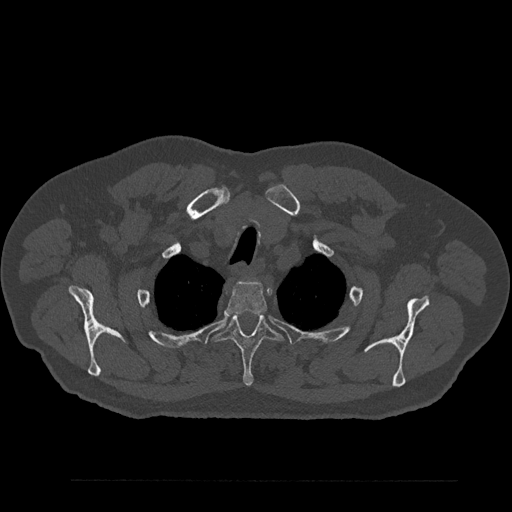
CT including the spine, one axial slice; position 695 of 797 along the scan axis; reconstruction kernel Br40s/3; 120 kVp; bone window (W 1800 / L 400 HU); 0.5 mm slice thickness; 512 × 512 image matrix, field of view 430 × 430 mm. Patient: male, 61 years. Case-level facts recorded for this patient, not image findings: primary cancer: prostate.
Structures marked on this image (semi-automatically segmented with operator editing):
- T2 vertebra: bounding box (x1, y1, x2, y2) in pixels: (225, 280, 268, 315)
- T3 vertebra: (215, 314, 282, 387)